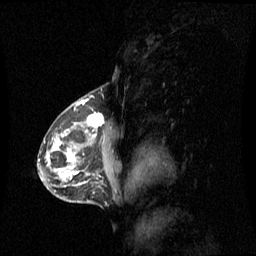
Breast MRI (dynamic contrast-enhanced), one sagittal slice. Slice 40 of 60 in the series (ordered by position). Dynamic contrast-enhanced series, image 2 of 3 at this slice position (ordered by acquisition). 1.5 T. TE 4.2 ms, TR 8.4 ms. 256 × 256 image matrix, field of view 270 × 270 mm. Patient: female, 42 years. From the clinical record (not read from this slice): setting: breast cancer imaged before/during neoadjuvant chemotherapy; receptor status: HR-positive, HER2-negative.
Outlined on this slice (semi-automatically segmented with operator editing):
- analysis volume of interest (the breast-tissue region the enhancement analysis was run in; not a lesion): bounding box [x1, y1, x2, y2] px = [56, 112, 120, 185]
- tumour enhancement mask (voxels above the 70 % enhancement threshold inside the analysis volume of interest): [59, 113, 104, 179]